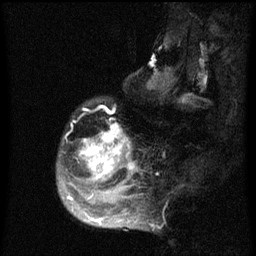
Breast MRI (dynamic contrast-enhanced), one sagittal slice; slice 16 of 60 in the series (ordered by position); dynamic contrast-enhanced series, image 2 of 3 at this slice position (ordered by acquisition); 1.5 T; TE 4.2 ms, TR 8 ms; 2 mm slice thickness; 256 × 256 image matrix, field of view 190 × 190 mm. Patient: female, 50 years.
Outlined on this slice (semi-automatic segmentation, software-assisted and operator-edited):
- analysis volume of interest (the breast-tissue region the enhancement analysis was run in; not a lesion): bounding box (x1, y1, x2, y2) in pixels: (57, 100, 142, 216)
- tumour enhancement mask (voxels above the 70 % enhancement threshold inside the analysis volume of interest): (67, 125, 134, 216)